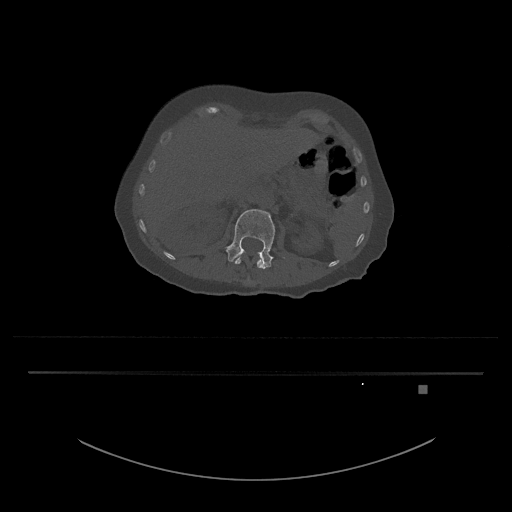
CT including the spine, one axial slice; slice 510 of 797 in the series (ordered by position); 120 kVp; bone window (W 1800 / L 400 HU); 0.5 mm slice thickness; 512 × 512 image matrix. Patient: female, 57 years. From the clinical record (not read from this slice): primary cancer: cervical.
Outlined on this slice (semi-automatic segmentation, software-assisted and operator-edited):
- L1 vertebra: bounding box <235,252,265,268> (left, top, right, bottom; pixels)